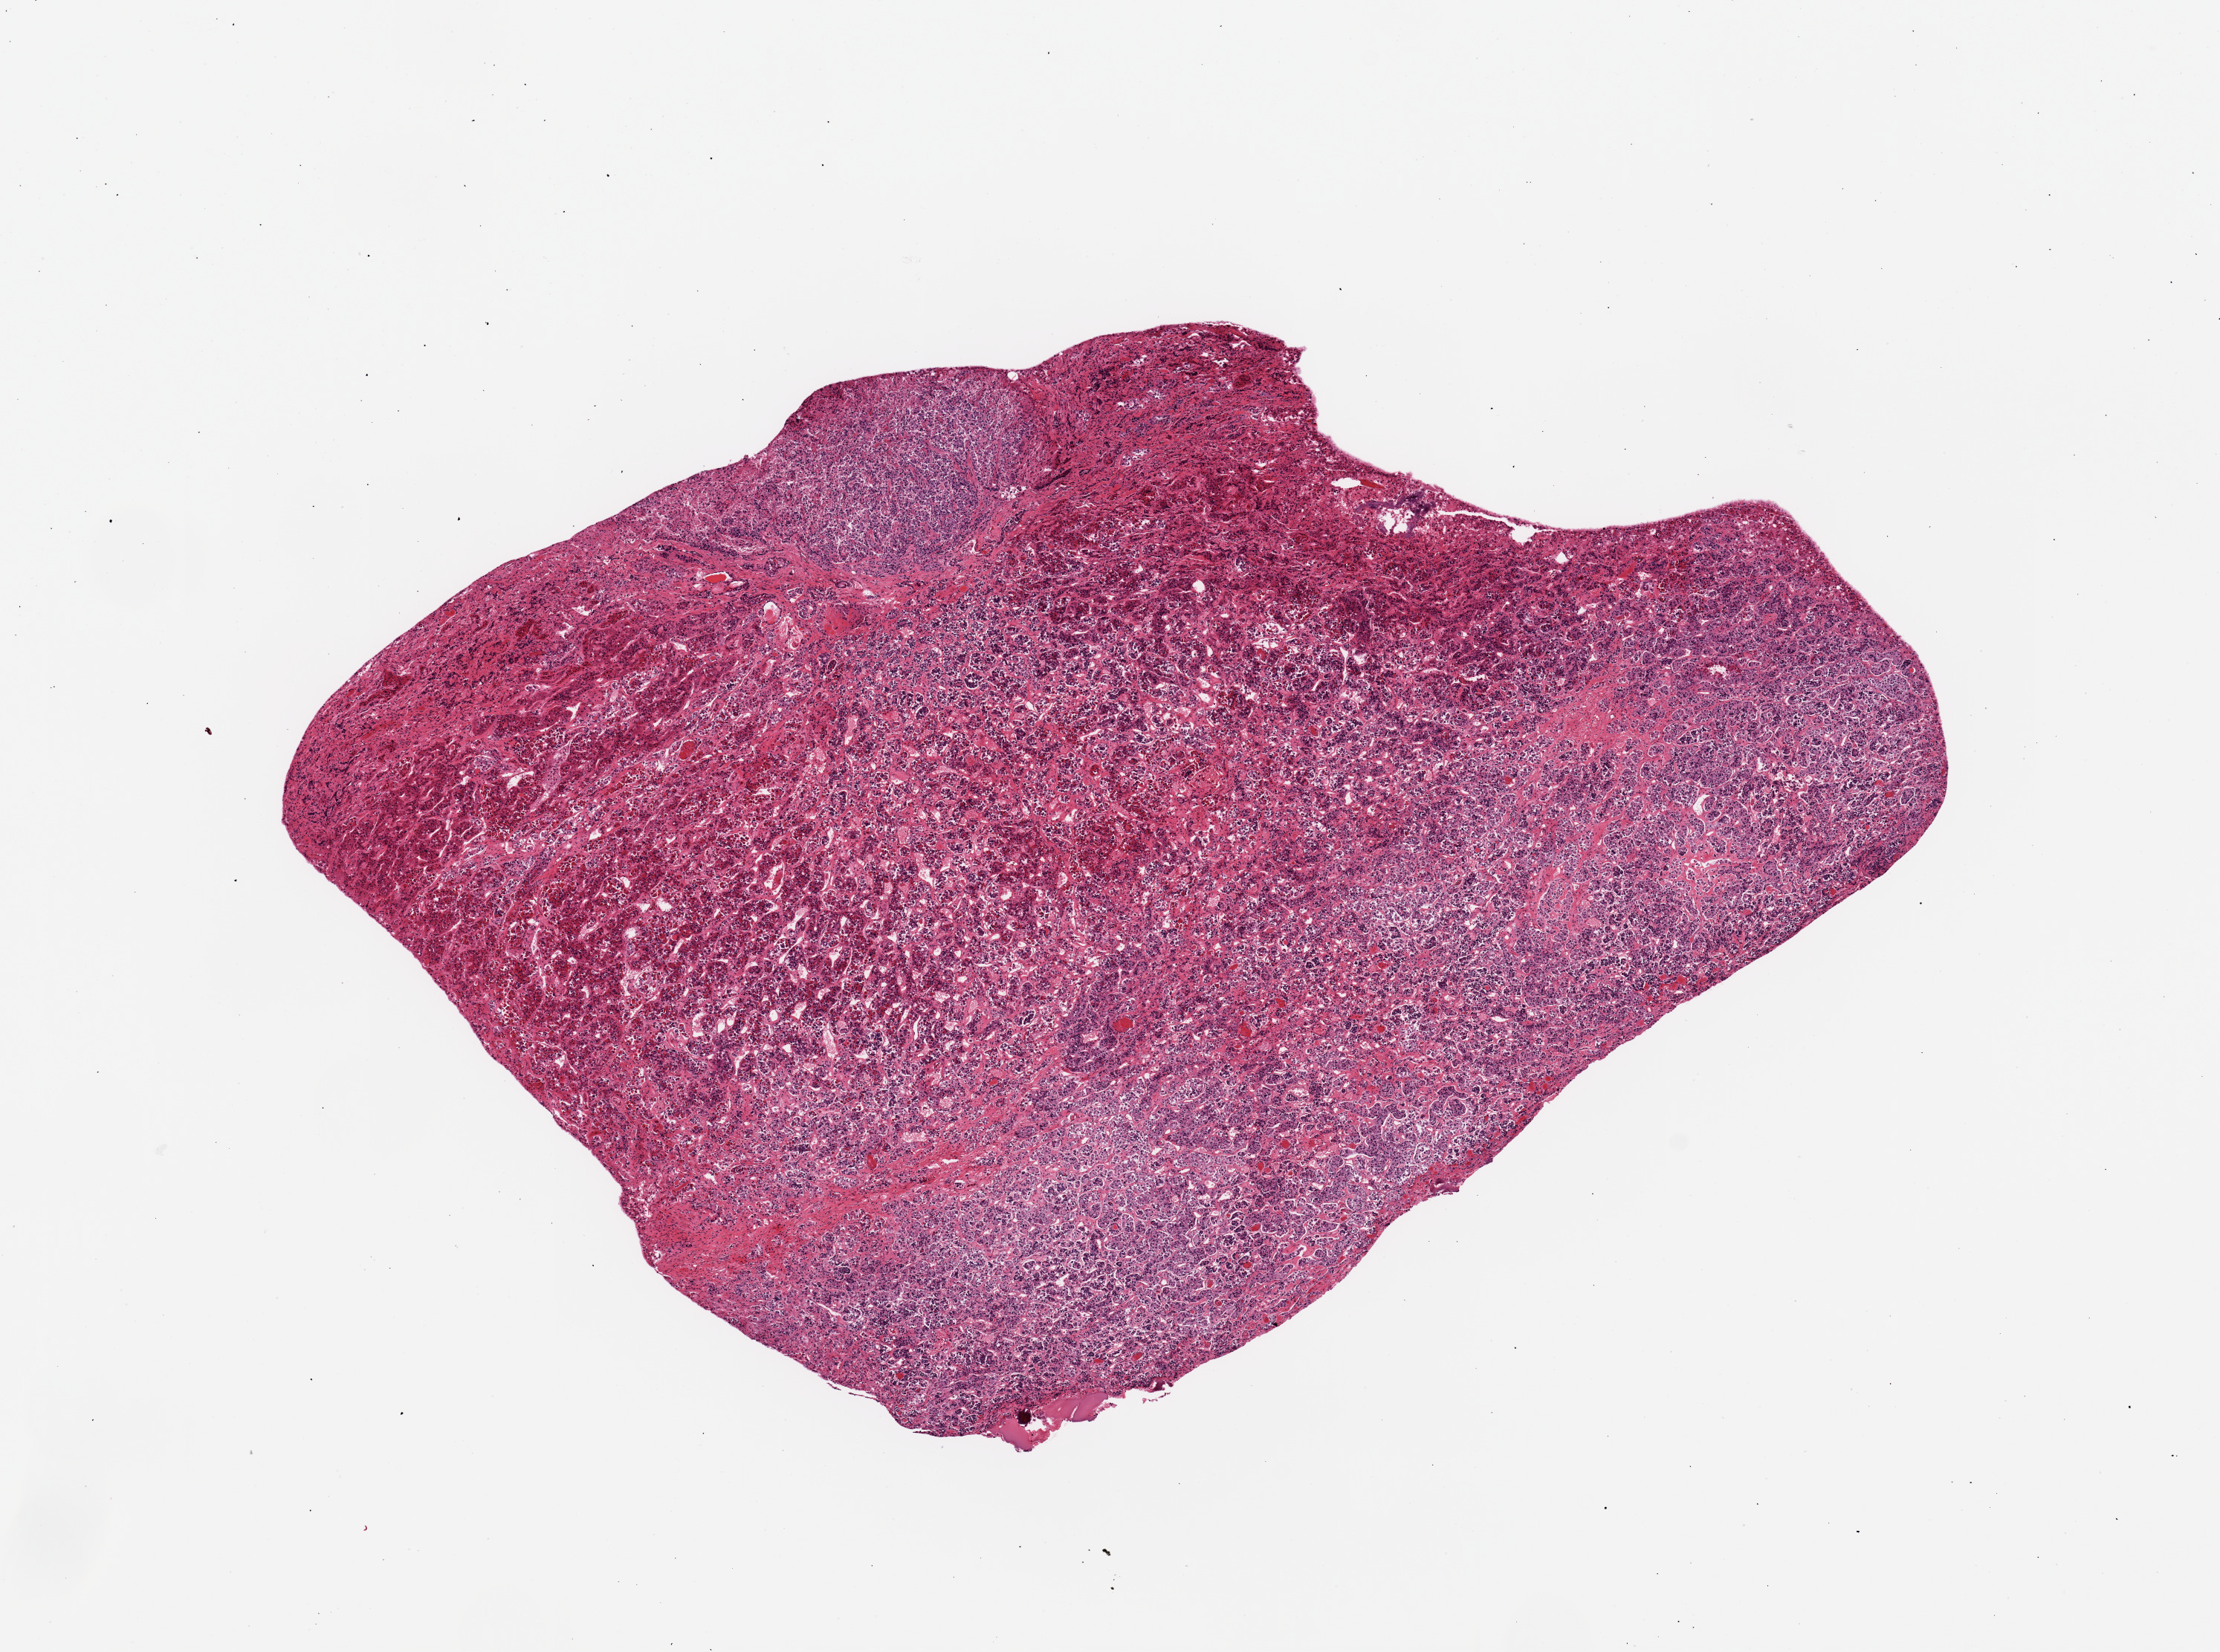
Digitized H&E-stained section — low-resolution overview of the scanned area, about 11.8 x 8.8 mm (from a 20x scan). PAXgene-fixed, paraffin-embedded tissue. Section of pituitary (target tissue). Donor tissue sample. Donor sex: male.
Pathologist's review note for this sample: 1 piece; anterior lobe.